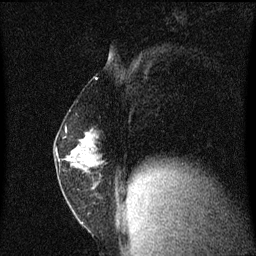
Breast MRI (dynamic contrast-enhanced), one sagittal slice; slice 28 of 60 in the series (ordered by position); dynamic contrast-enhanced series, image 2 of 3 at this slice position (ordered by acquisition); 1.5 T; TE 4.2 ms, TR 8.4 ms; 2 mm slice thickness; 256 × 256 image matrix. Patient: female, 52 years. Case-level facts recorded for this patient, not image findings: setting: breast cancer imaged before/during neoadjuvant chemotherapy; receptor status: HER2-positive.
Outlined on this slice (semi-automatically segmented with operator editing):
- analysis volume of interest (the breast-tissue region the enhancement analysis was run in; not a lesion): bounding box [x1, y1, x2, y2] px = [55, 124, 119, 191]
- tumour enhancement mask (voxels above the 70 % enhancement threshold inside the analysis volume of interest): [70, 132, 92, 157]